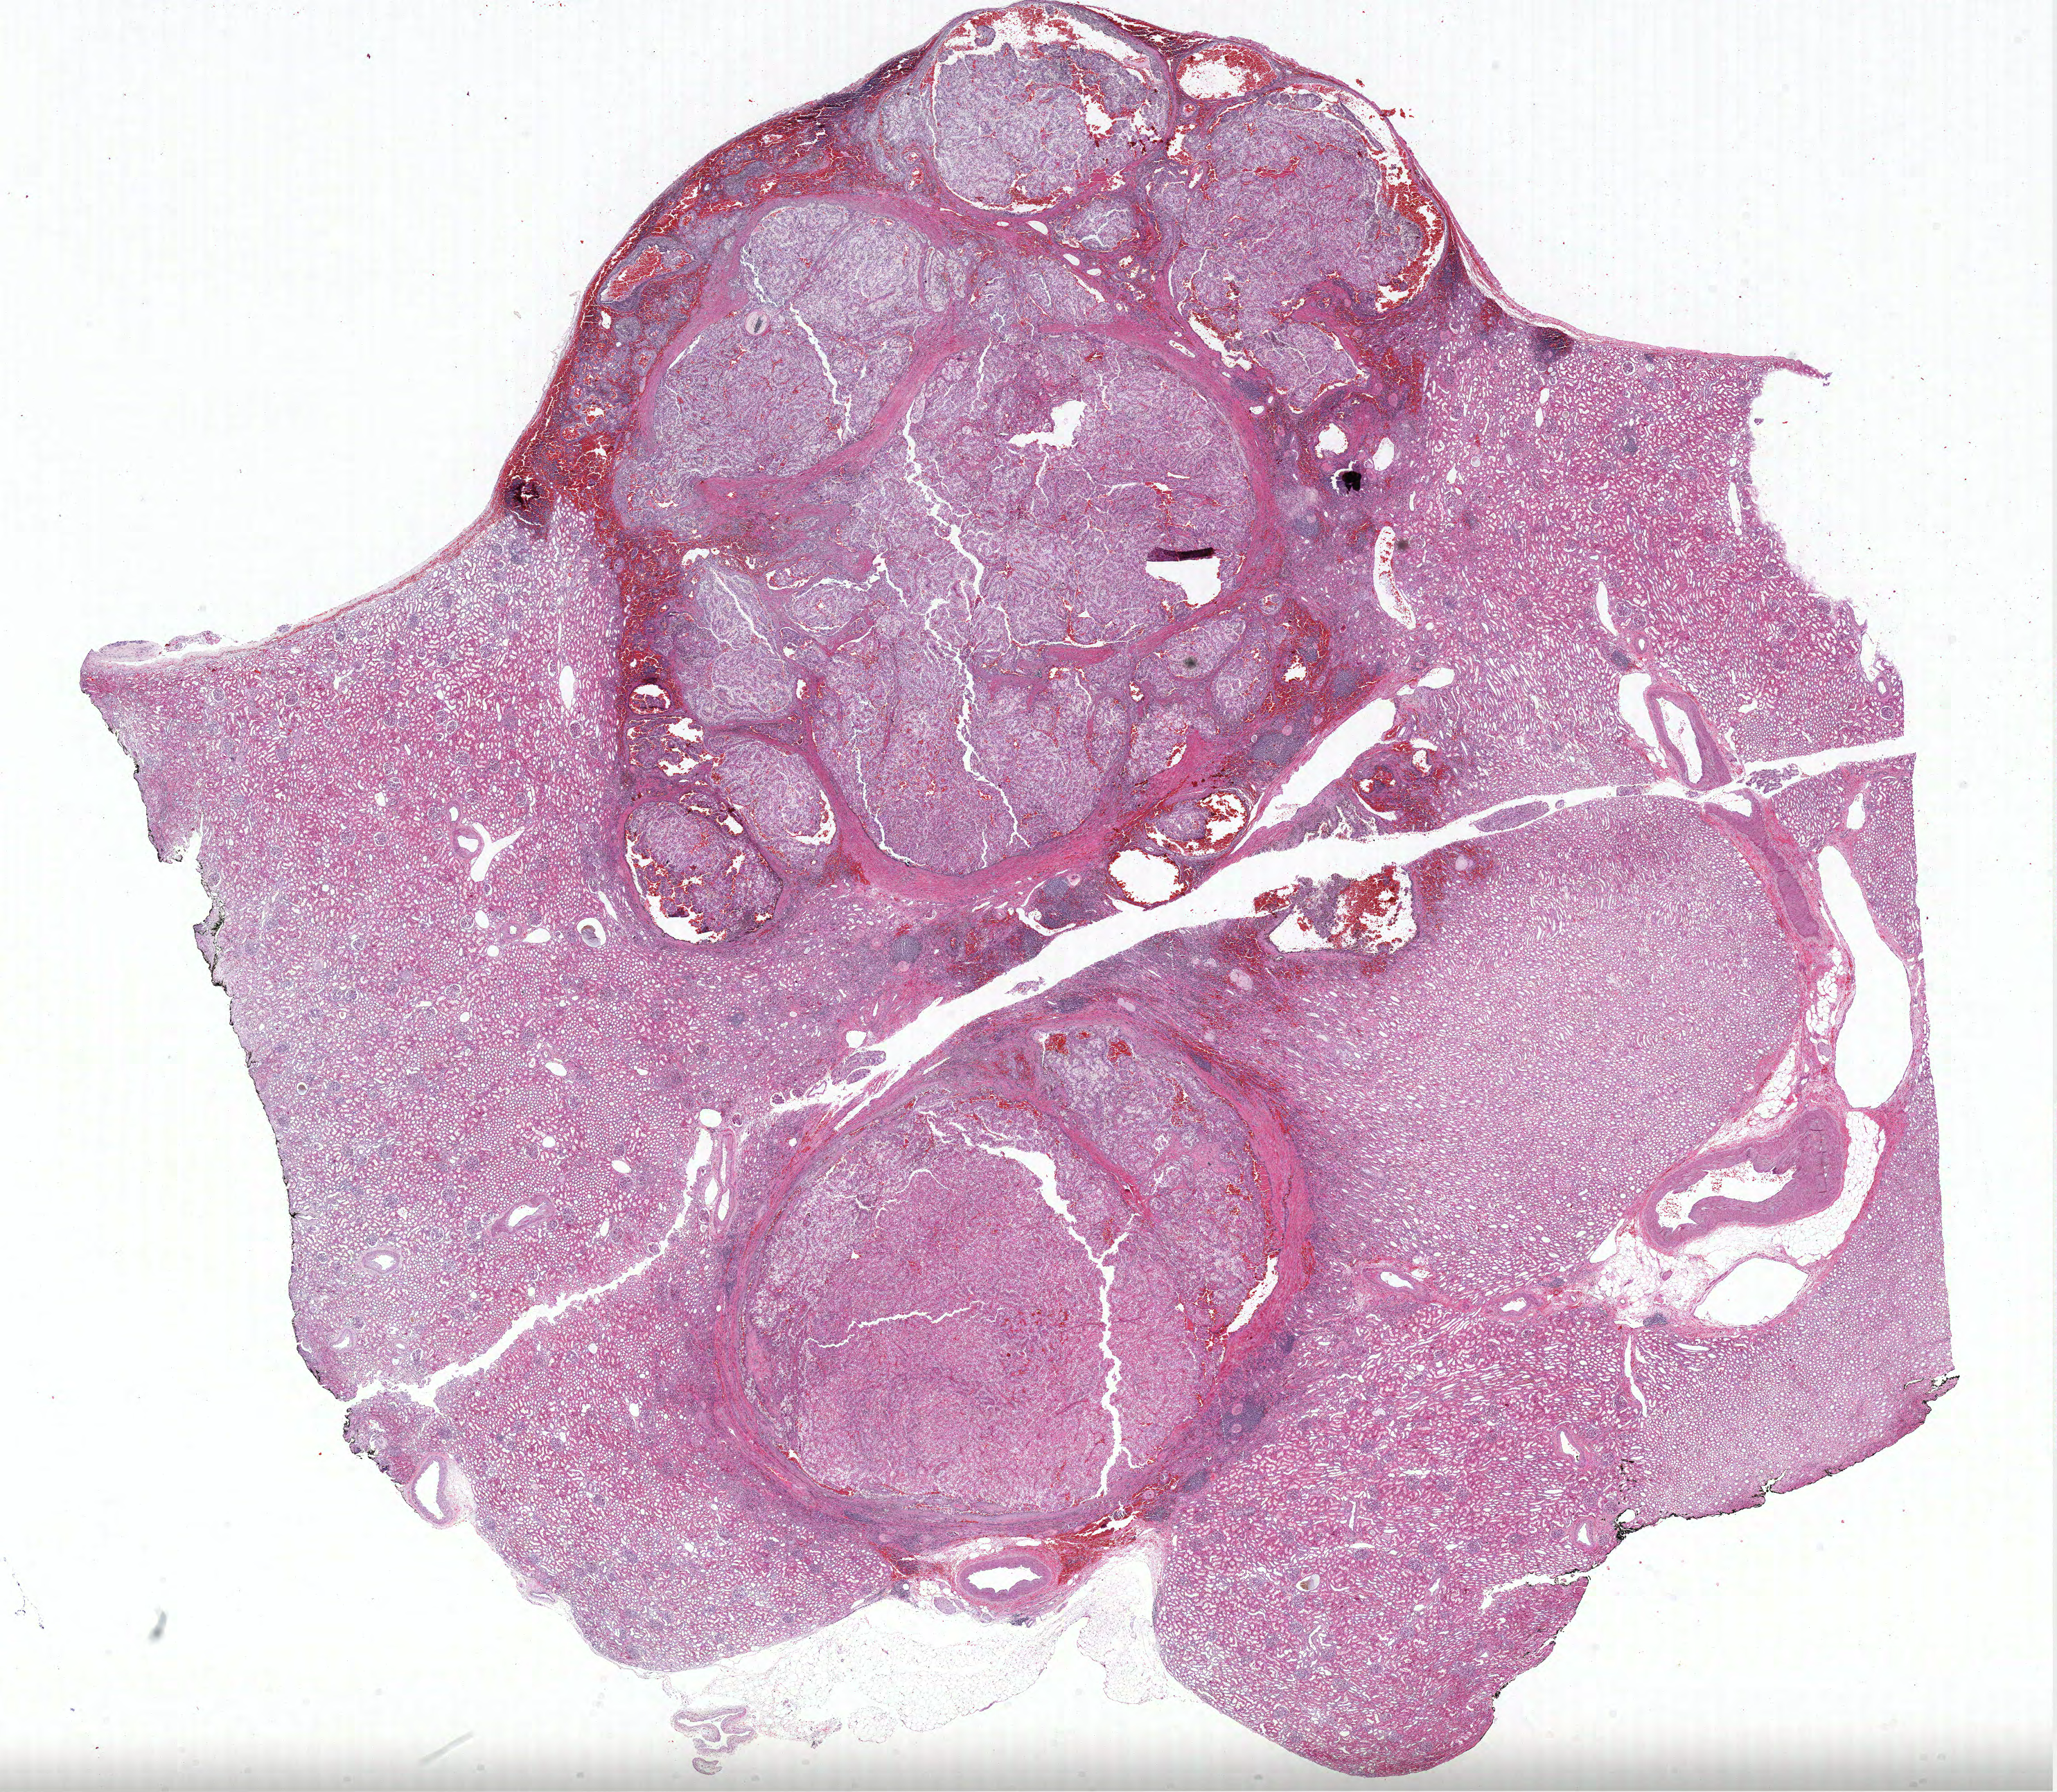
H&E-stained whole-slide image — whole scanned area (about 23.7 x 20.7 mm, acquisition: 40x scan) shown as a low-resolution overview; formalin-fixed paraffin-embedded (FFPE) diagnostic section; sample: primary tumour, kidney. Female, age 53 years at initial diagnosis.
* laterality: left
* histologic diagnosis: Papillary adenocarcinoma, NOS
* AJCC pathologic stage: I (6th edition)